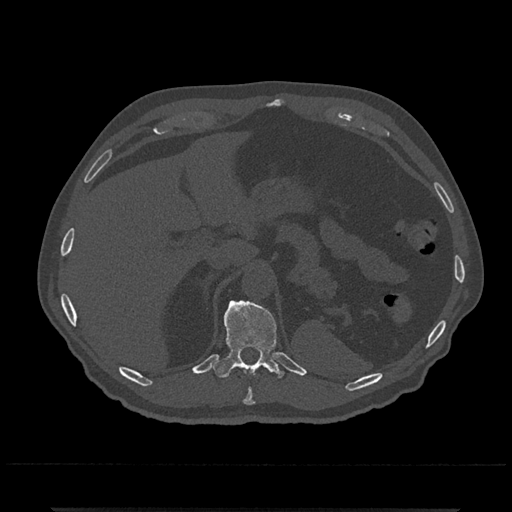
CT including the spine, one axial slice; reconstruction kernel Br40s/3; 120 kVp; bone window (W 1800 / L 400 HU); 0.5 mm slice thickness; 512 × 512 image matrix, field of view 393 × 393 mm. Patient: male, 67 years. From the clinical record (not read from this slice): primary cancer: prostate.
Annotated regions visible in this slice (semi-automatically segmented with operator editing):
- T10 vertebra: bounding box <243,389,254,405> (left, top, right, bottom; pixels)
- T11 vertebra: <212,300,285,378>